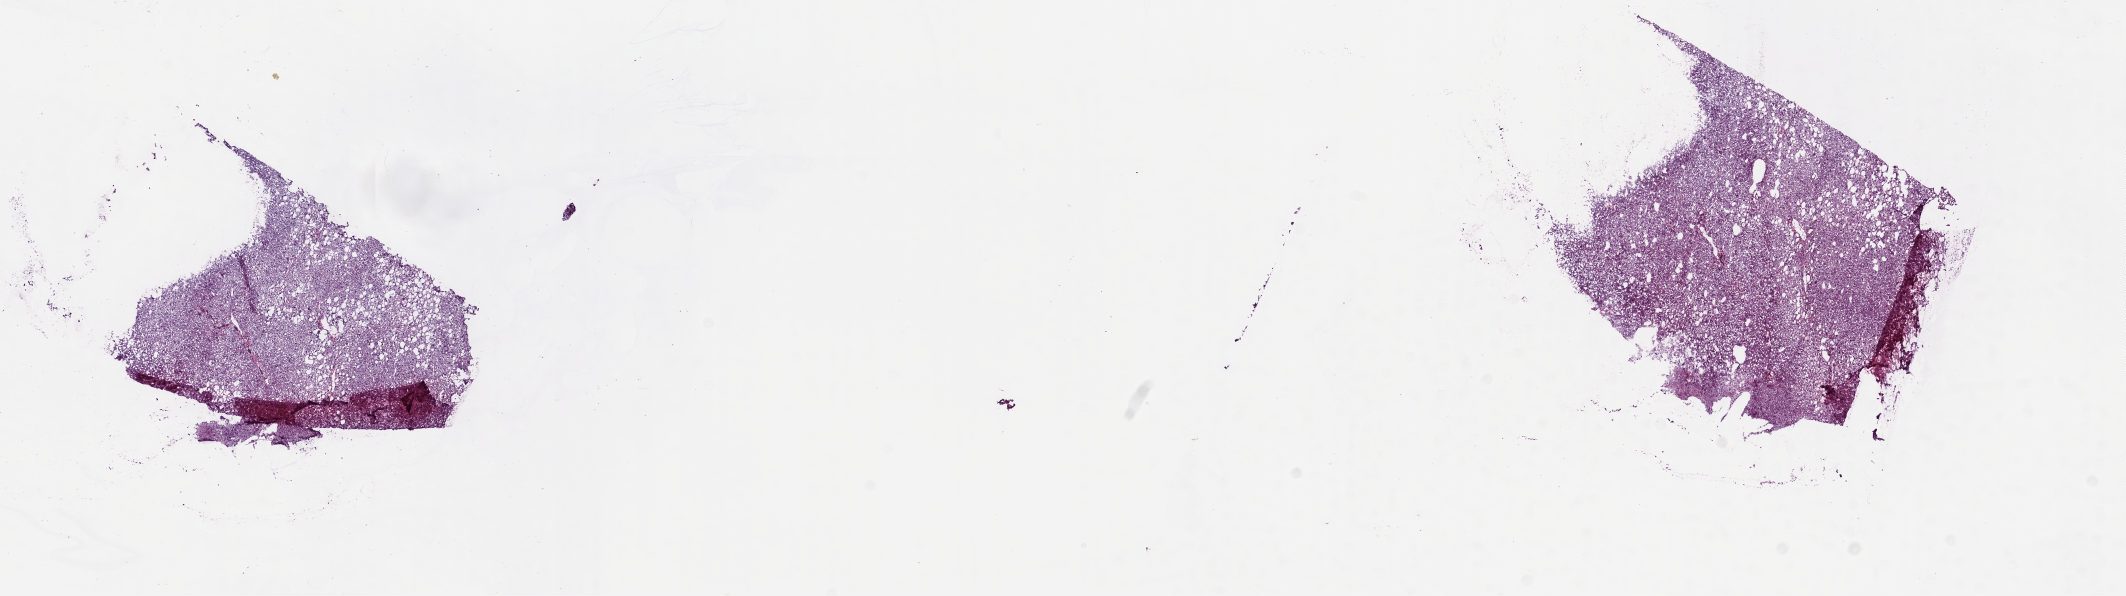
Whole-slide histology image, H&E — low-resolution overview of the scanned area, about 16.9 x 4.7 mm (from a 20x scan). Frozen section from the top of the tissue portion. Bile duct, solid tissue normal (non-tumour tissue) sample. Female patient; age at initial diagnosis 75 years. Composition of this section per pathologist review: tumour cells 0%, tumour nuclei 0%, normal cells 100%, stromal cells 0%, necrosis 0%. Inflammatory infiltration, as recorded: lymphocyte infiltration 2%, monocyte infiltration 0%, neutrophil infiltration 0%.
This section: solid tissue normal (non-tumour) sample from the same patient. Patient diagnosis: Cholangiocarcinoma (intrahepatic bile duct).